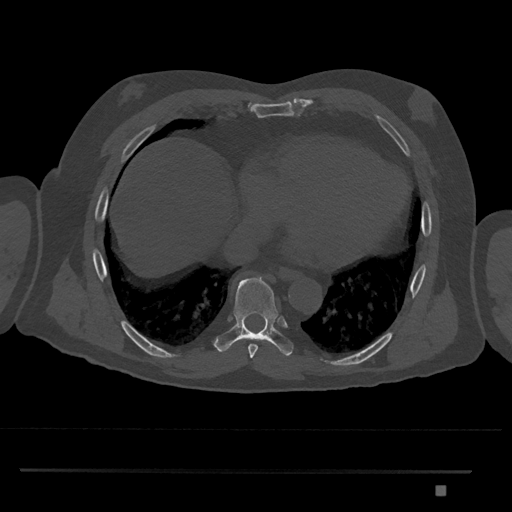
CT including the spine, one axial slice; slice 1122 of 1134 in the series (ordered by position); reconstruction kernel Br40s/3; bone window (W 1800 / L 400 HU); 0.5 mm slice thickness; 512 × 512 image matrix. Male patient, age 65 years. From the clinical record (not read from this slice): primary cancer: prostate.
Structures marked on this image (semi-automatically segmented with operator editing):
- T8 vertebra: box from (x=213, y=276) to (x=294, y=356) px